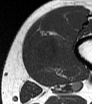
MRI of an extremity soft-tissue mass, one axial slice. Slice 12 of 62 in the series (ordered by position). MR volume resampled by the dataset authors to the PET/CT grid (not the native acquisition matrix). 3.27 mm slice thickness. 92 × 104 image matrix. Male patient. From the clinical record (not read from this slice): histological type: mixoid liposarcoma; grade: low; site of the primary tumour: left thigh.
Structures marked on this image (expert contour drawn on MRI and transferred to this co-registered scan by the dataset authors):
- gross tumour volume (mass): bounding box (x1, y1, x2, y2) in pixels: (34, 38, 58, 64)